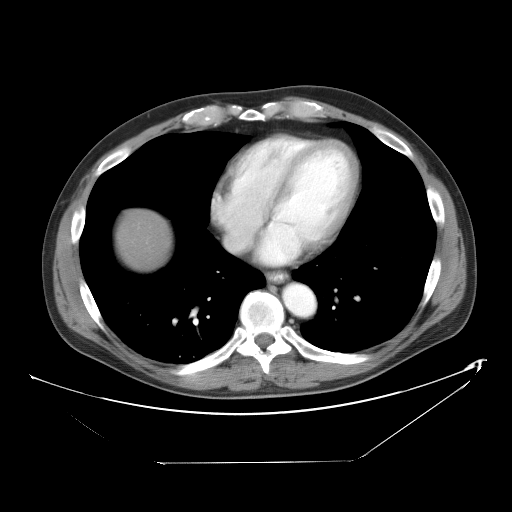
Contrast-enhanced abdominal CT, one axial slice. 120 kVp. Intravenous contrast given. Soft-tissue window (W 400 / L 40 HU). 5 mm slice thickness. 512 × 512 image matrix, field of view 438 × 438 mm. Male patient, age 59 years. Case-level facts recorded for this patient, not image findings: diagnosis: colorectal cancer liver metastases, imaged before liver resection; multiple liver metastases: yes; largest metastasis: 8.5 cm.
Outlined on this slice (outlined manually by an expert reader):
- liver: bounding box [x1, y1, x2, y2] px = [121, 214, 170, 266]
- planned liver remnant (the part of the liver to remain after resection): [122, 213, 170, 267]